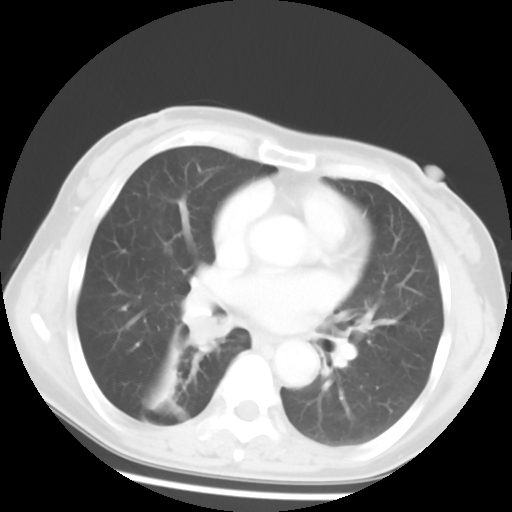
Chest CT, one axial slice; slice 27 of 52 in the series (ordered by position); 120 kVp; lung window (W 1500 / L -600 HU); 512 × 512 image matrix, field of view 297 × 297 mm. Patient: female, 54 years. From the clinical record (not read from this slice): clinical TNM (as recorded): T1c N0 M0; histopathological grade: G1-2.
Outlined on this slice (bounding box drawn by a radiologist):
- lung tumour (recorded histology: squamous cell carcinoma): bounding box (x1, y1, x2, y2) in pixels: (175, 286, 232, 353)